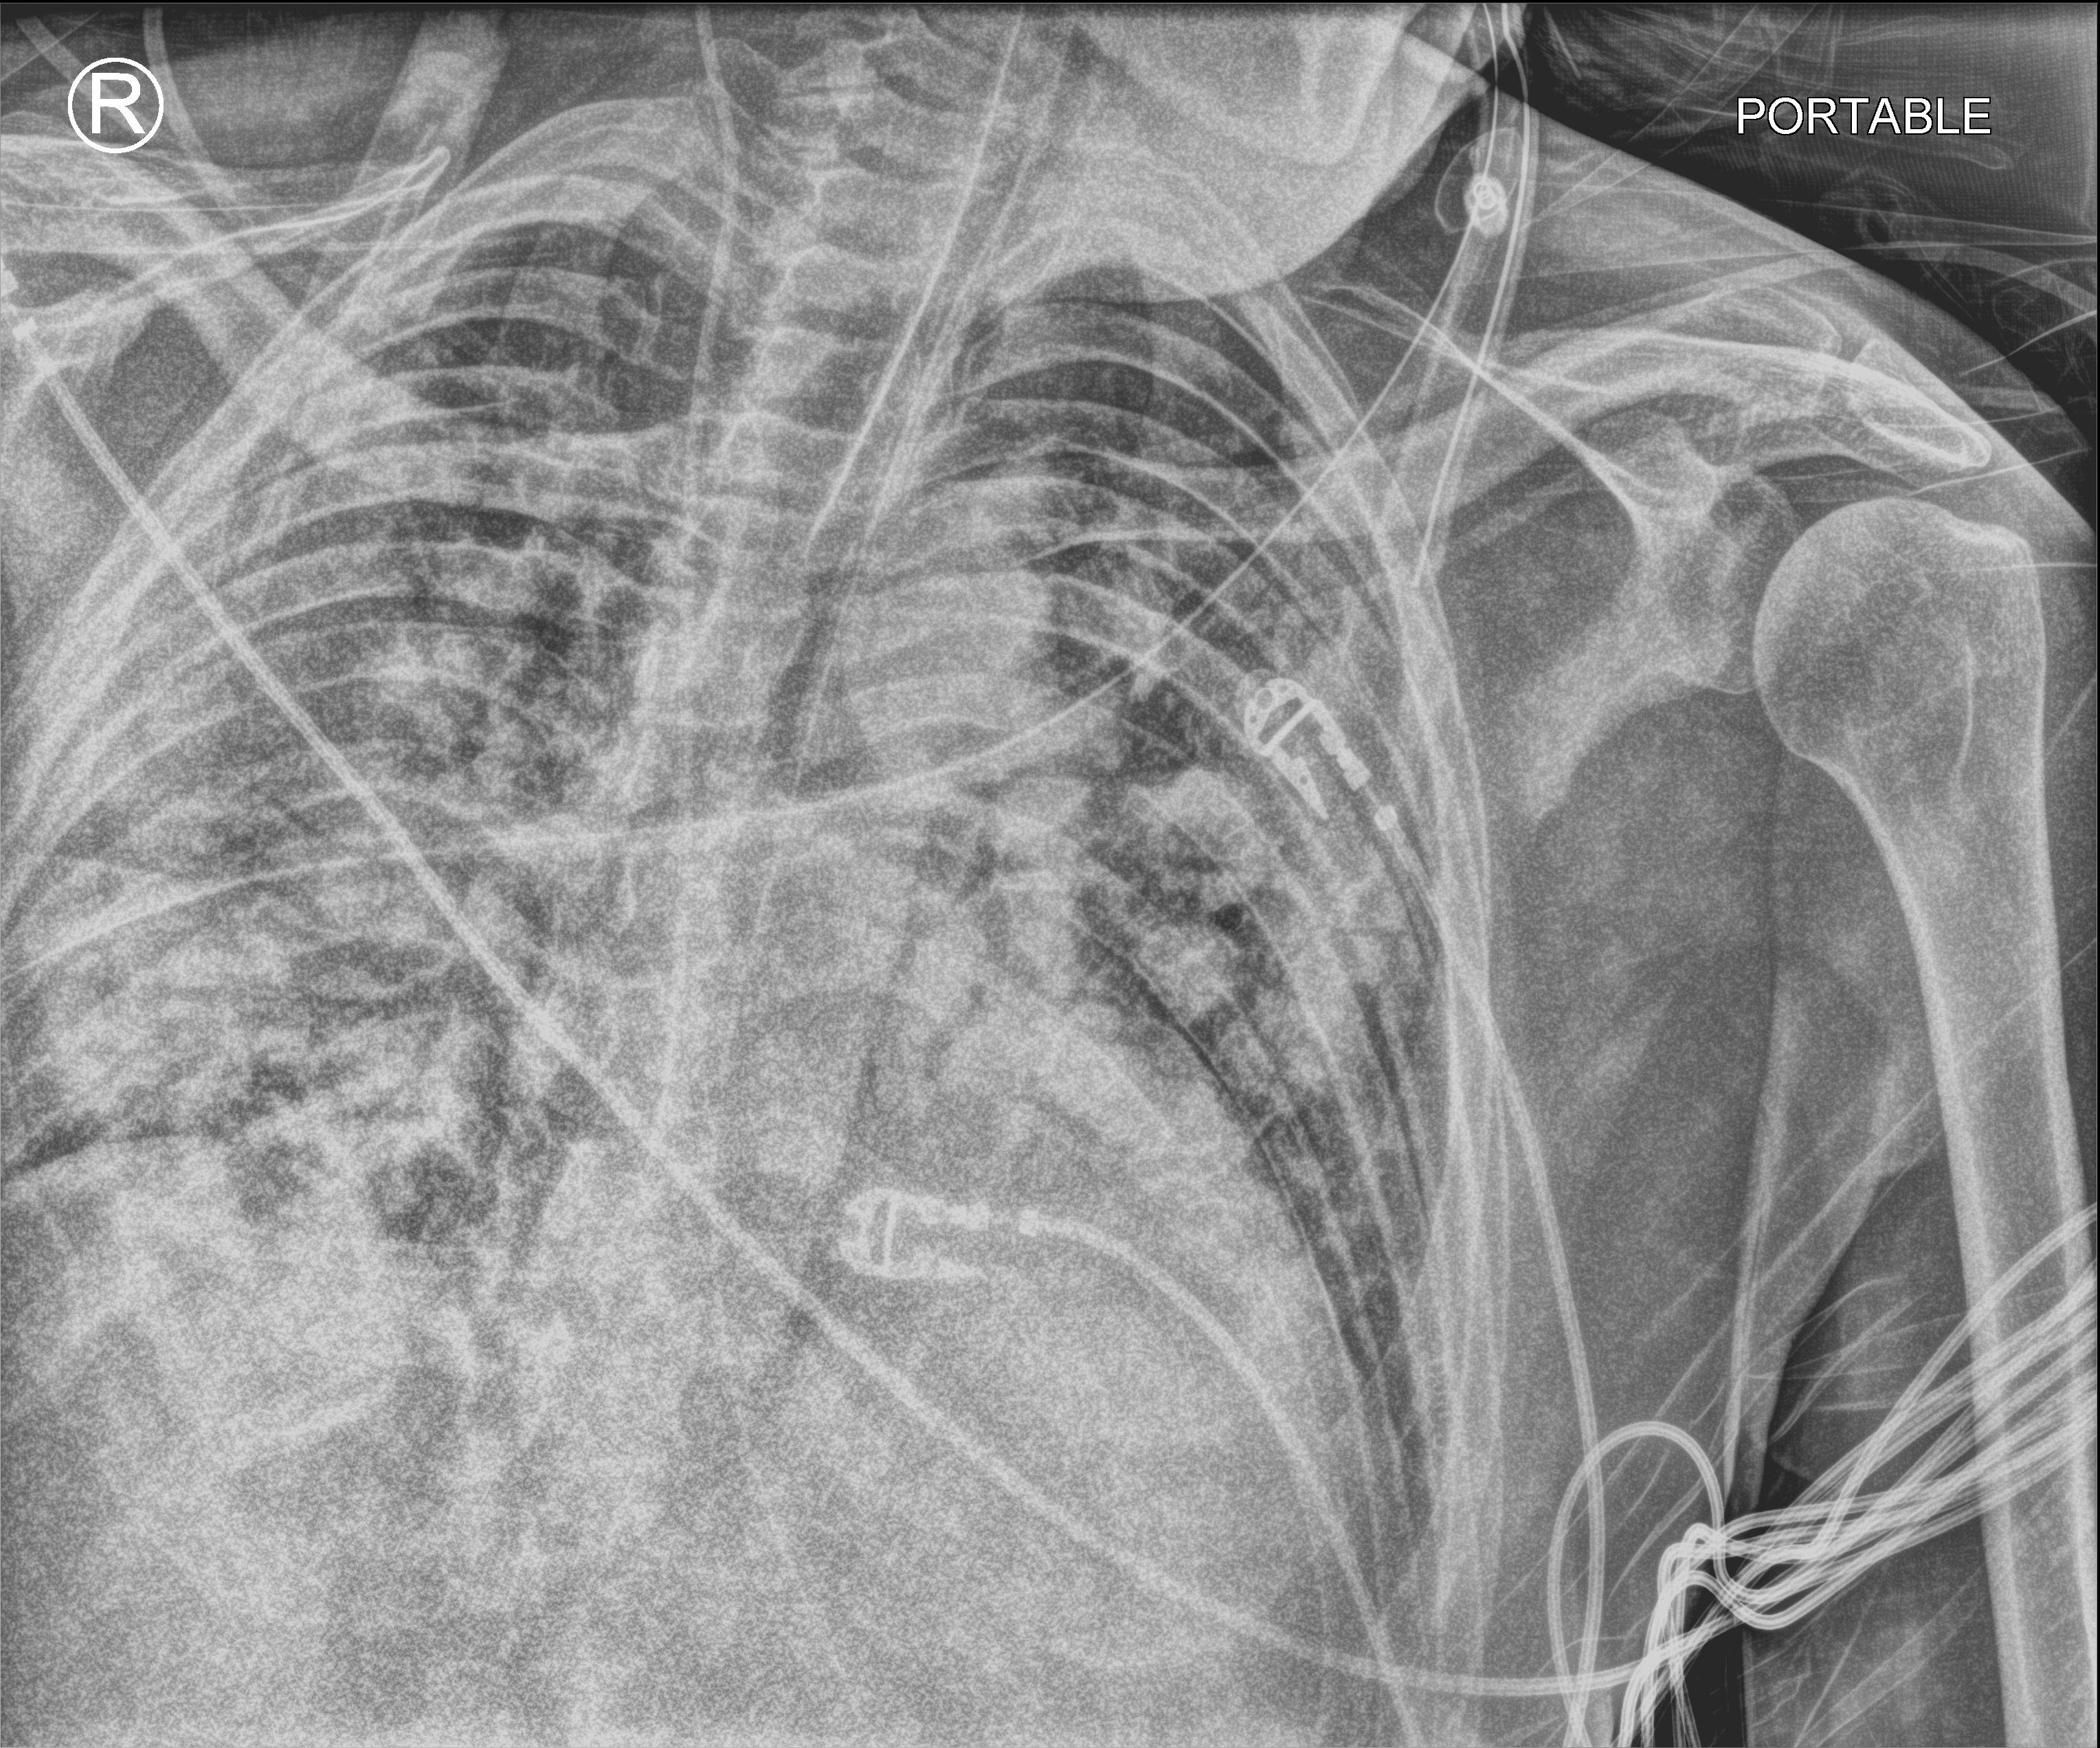
Portable chest radiograph; anteroposterior (AP) projection. Male patient hospitalised with COVID-19, age 18–59 years.
Admission-level facts for this patient (not findings on this image; timing relative to this image not recorded): length of hospital stay: 75 days; mechanically ventilated during this hospital stay: yes; admitted to intensive care during this hospital stay: yes.